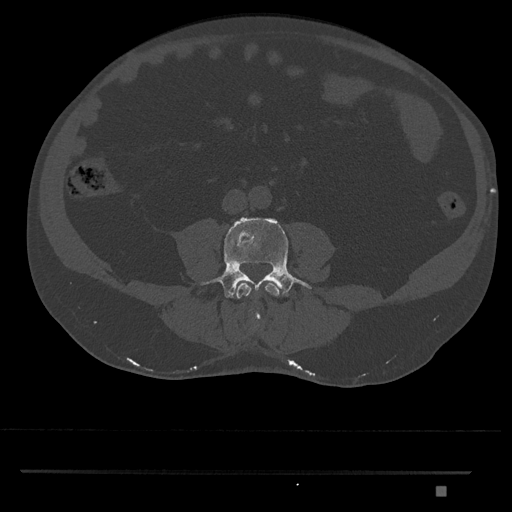
CT including the spine, one axial slice. Position 634 of 1134 along the scan axis. Reconstruction kernel Br40s/3. 120 kVp. Bone window (W 1800 / L 400 HU). 0.5 mm slice thickness. 512 × 512 image matrix. Patient: male, 65 years. From the clinical record (not read from this slice): primary cancer: prostate.
Structures marked on this image (semi-automatic segmentation, software-assisted and operator-edited):
- L3 vertebra: bounding box (x1, y1, x2, y2) in pixels: (236, 282, 280, 323)
- L4 vertebra: (201, 217, 311, 298)